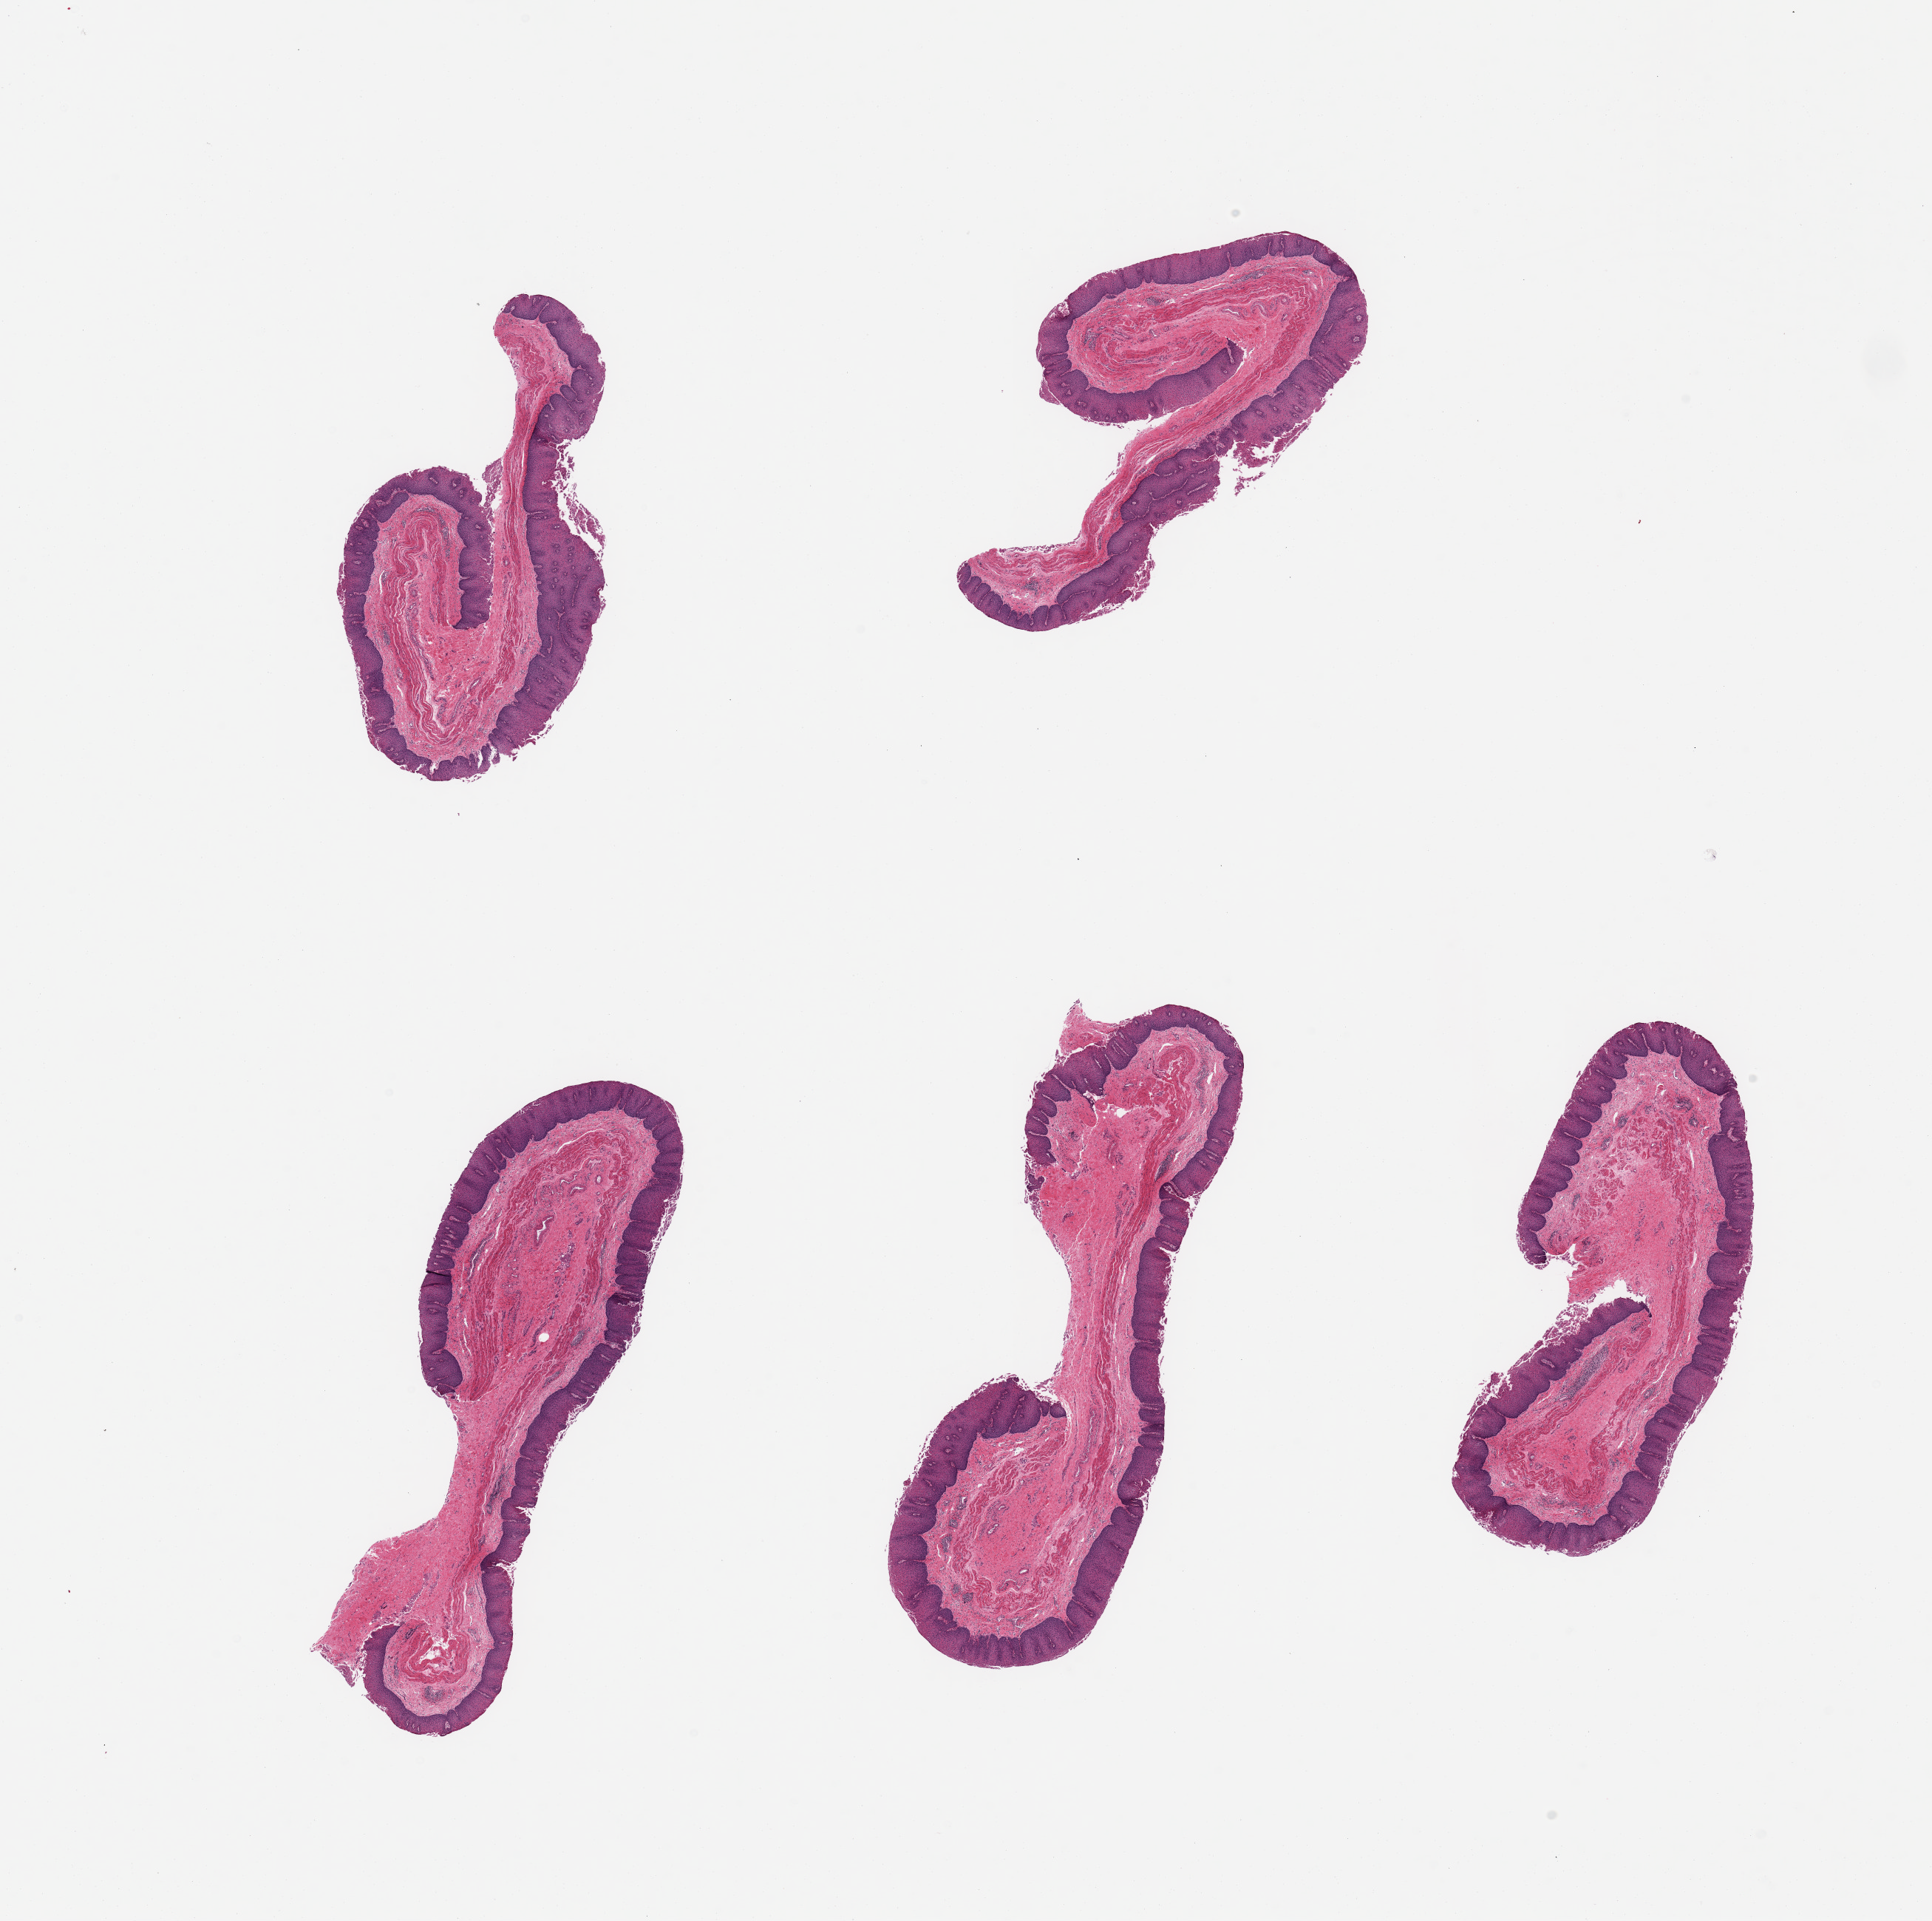
Digitized haematoxylin and eosin-stained section, low-resolution overview of the scanned area, about 20.7 x 20.6 mm, PAXgene-fixed, paraffin-embedded tissue, section of esophageal mucous membrane (target tissue), tissue donor sample. Donor: male.
• reviewer comment on this tissue sample: 5 pieces, Squamous mucosa is ~0.4mm, ~25-30% thickness approaching score 2, surface sloughing